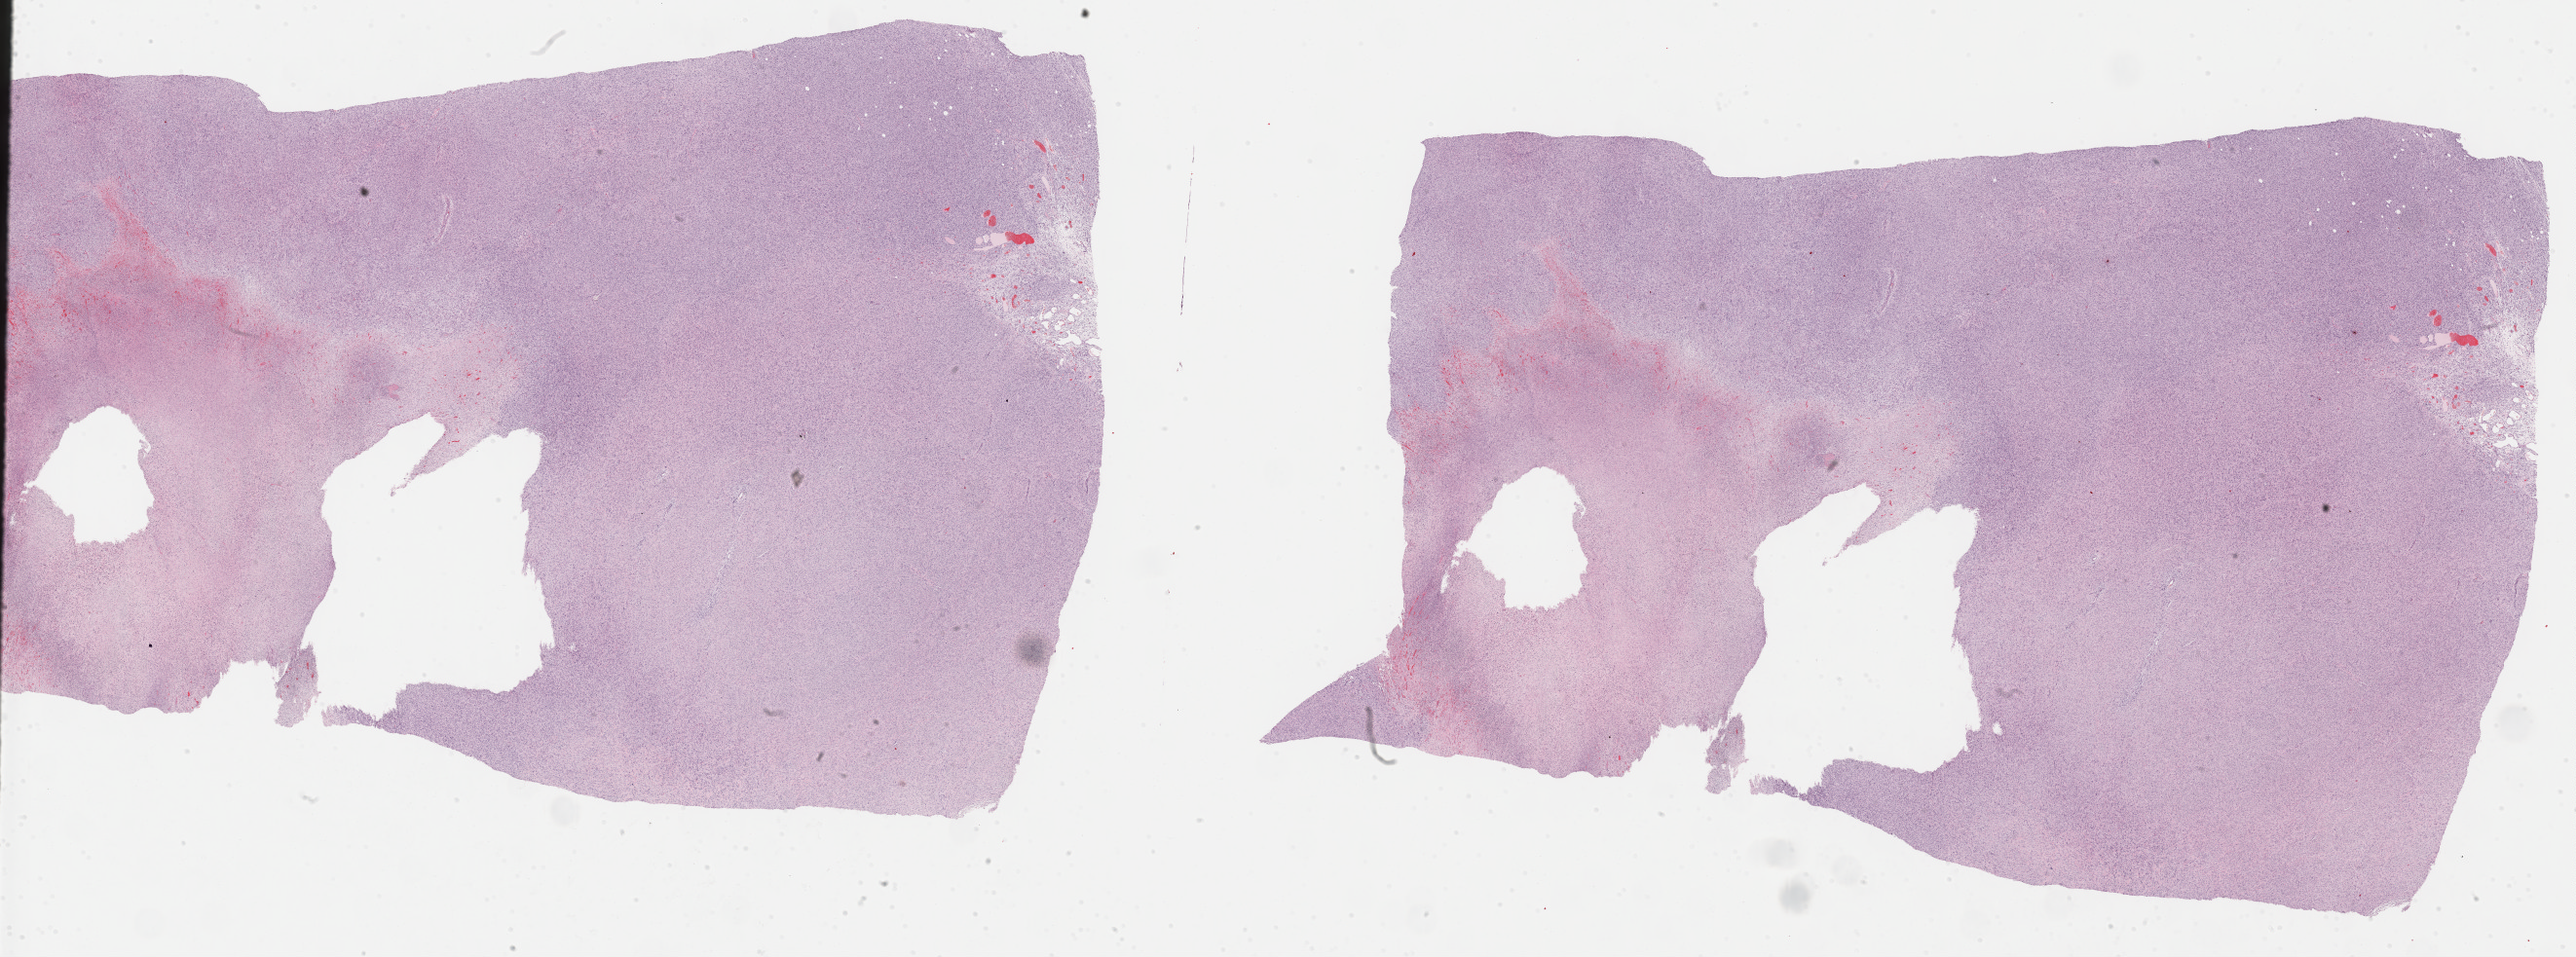
Hematoxylin and eosin (H&E) stained whole-slide image — whole scanned area (about 42.8 x 15.9 mm) shown as a low-resolution overview, formalin-fixed paraffin-embedded (FFPE) diagnostic section, primary tumour sample from the connective, subcutaneous and other soft tissues. Female patient; age at initial diagnosis 63 years.
Diagnosis: Malignant fibrous histiocytoma (connective, subcutaneous and other soft tissues of thorax).